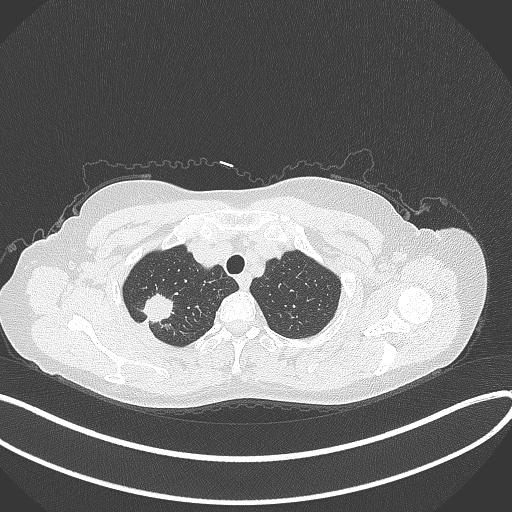
Chest CT, one axial slice. Position 315 of 337 along the scan axis. Lung window (W 1500 / L -600 HU). 512 × 512 image matrix. Patient: female, 50 years. From the clinical record (not read from this slice): clinical TNM (as recorded): T1c N0 M0.
Annotated regions visible in this slice (rectangle marked by the reading radiologist):
- lung tumour (recorded histology: adenocarcinoma): bounding box <135,293,178,327> (left, top, right, bottom; pixels)